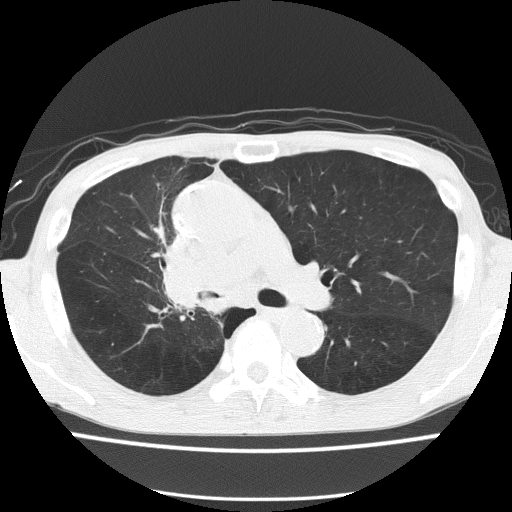
Low-dose screening chest CT, one axial slice. Slice 93 of 150 in the series (ordered by position). Reconstruction kernel FC51. 120 kVp. Lung window (W 1500 / L -600 HU). 512 × 512 image matrix.
Outlined on this slice (manually delineated by an expert):
- lesion 1 (tumor, hilum of right lung): bounding box <167,238,228,313> (left, top, right, bottom; pixels)